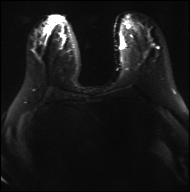
Breast MRI, one axial slice; position 11 of 36 along the scan axis; diffusion-weighted series; image 2 of 4 stored at this slice position (different b-values; order by instance number); 3 T; 190 × 192 image matrix, field of view 317 × 320 mm. Female patient.
Structures marked on this image (manually delineated by an expert):
- tumour on diffusion-weighted imaging: bounding box (x1, y1, x2, y2) in pixels: (77, 23, 82, 26)